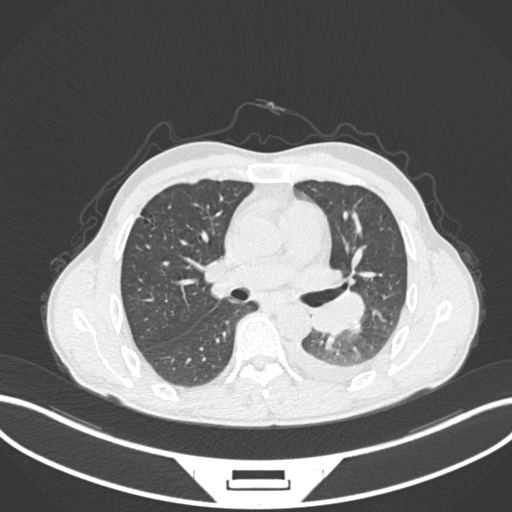
Chest CT, one axial slice; position 140 of 222 along the scan axis; reconstruction kernel B30f; lung window (W 1500 / L -600 HU); 1 mm slice thickness; 512 × 512 image matrix, field of view 400 × 400 mm. Patient: male, 47 years. From the clinical record (not read from this slice): clinical TNM (as recorded): T3 N1 M1c; histopathological grade: G3.
Annotated regions visible in this slice (rectangle marked by the reading radiologist):
- lung tumour (recorded histology: small cell carcinoma): bounding box [x1, y1, x2, y2] px = [305, 290, 368, 335]